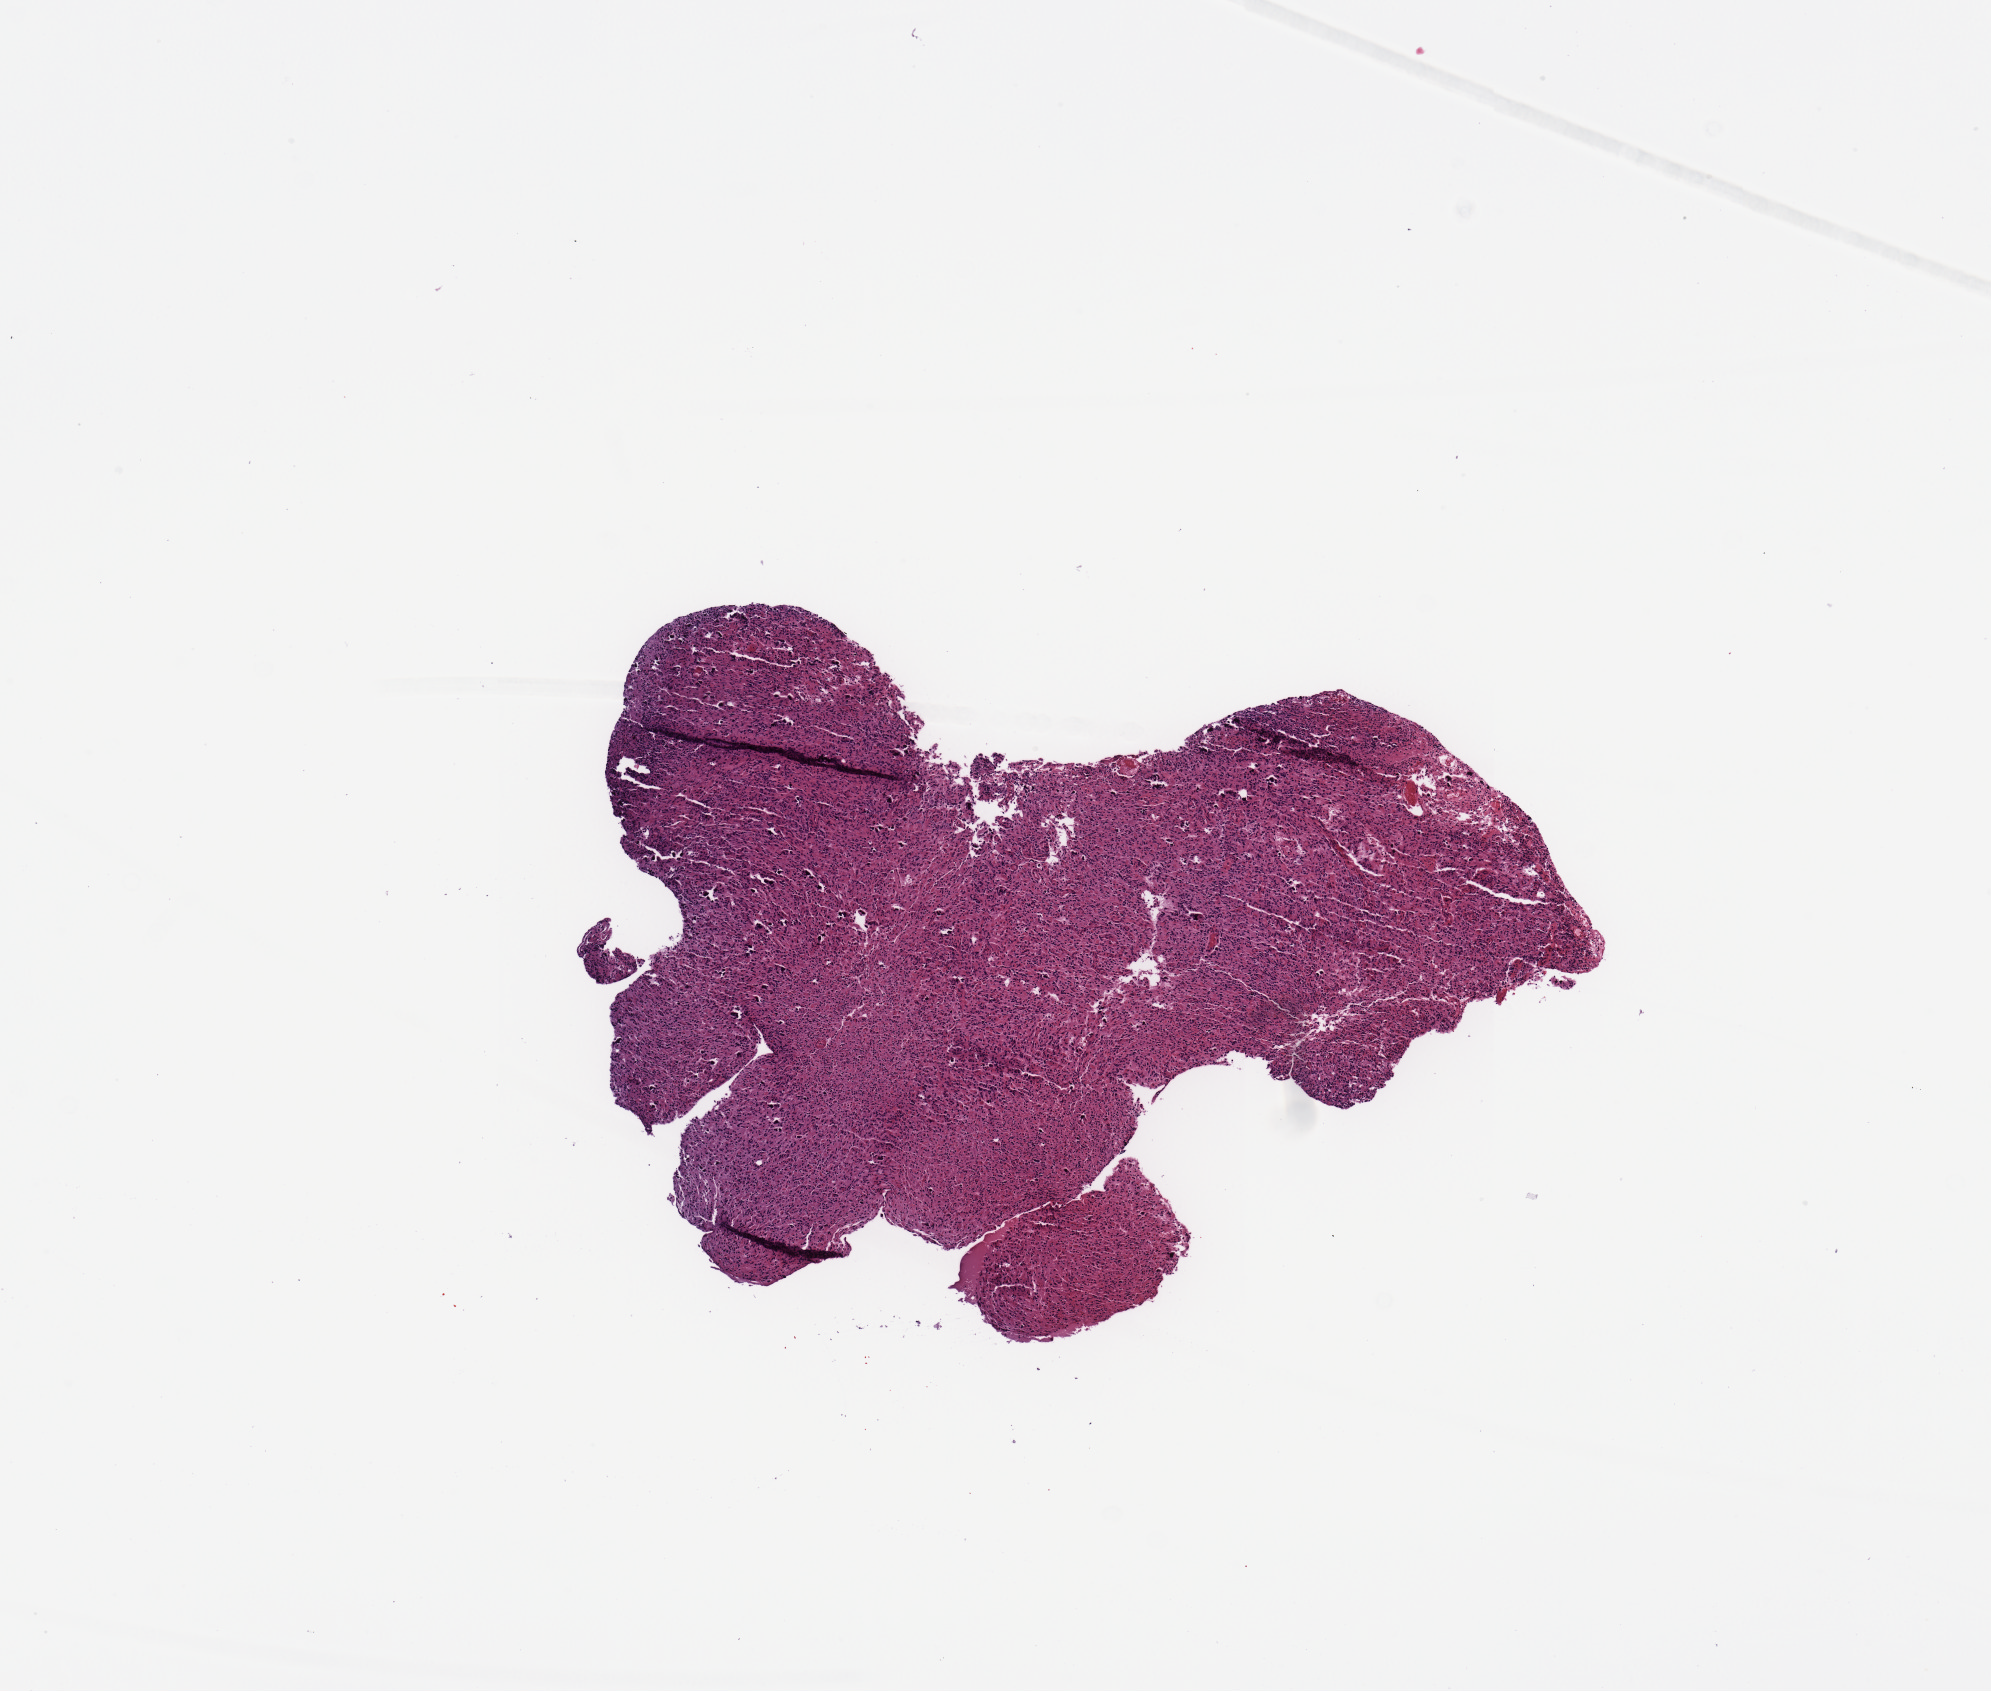
Digitized H&E-stained tissue section (whole slide) — a low-resolution overview of the entire scanned area, about 7.9 x 6.7 mm (from a 20x scan). Tumour tissue sample, sampled site: frontal lobe. Patient: female, age 59 years. Pathologist review of this section (percent, as recorded): tumour nuclei 85%, necrosis 5%.
Primary tumour site (as recorded): frontal lobe. Diagnosis: Glioblastoma.